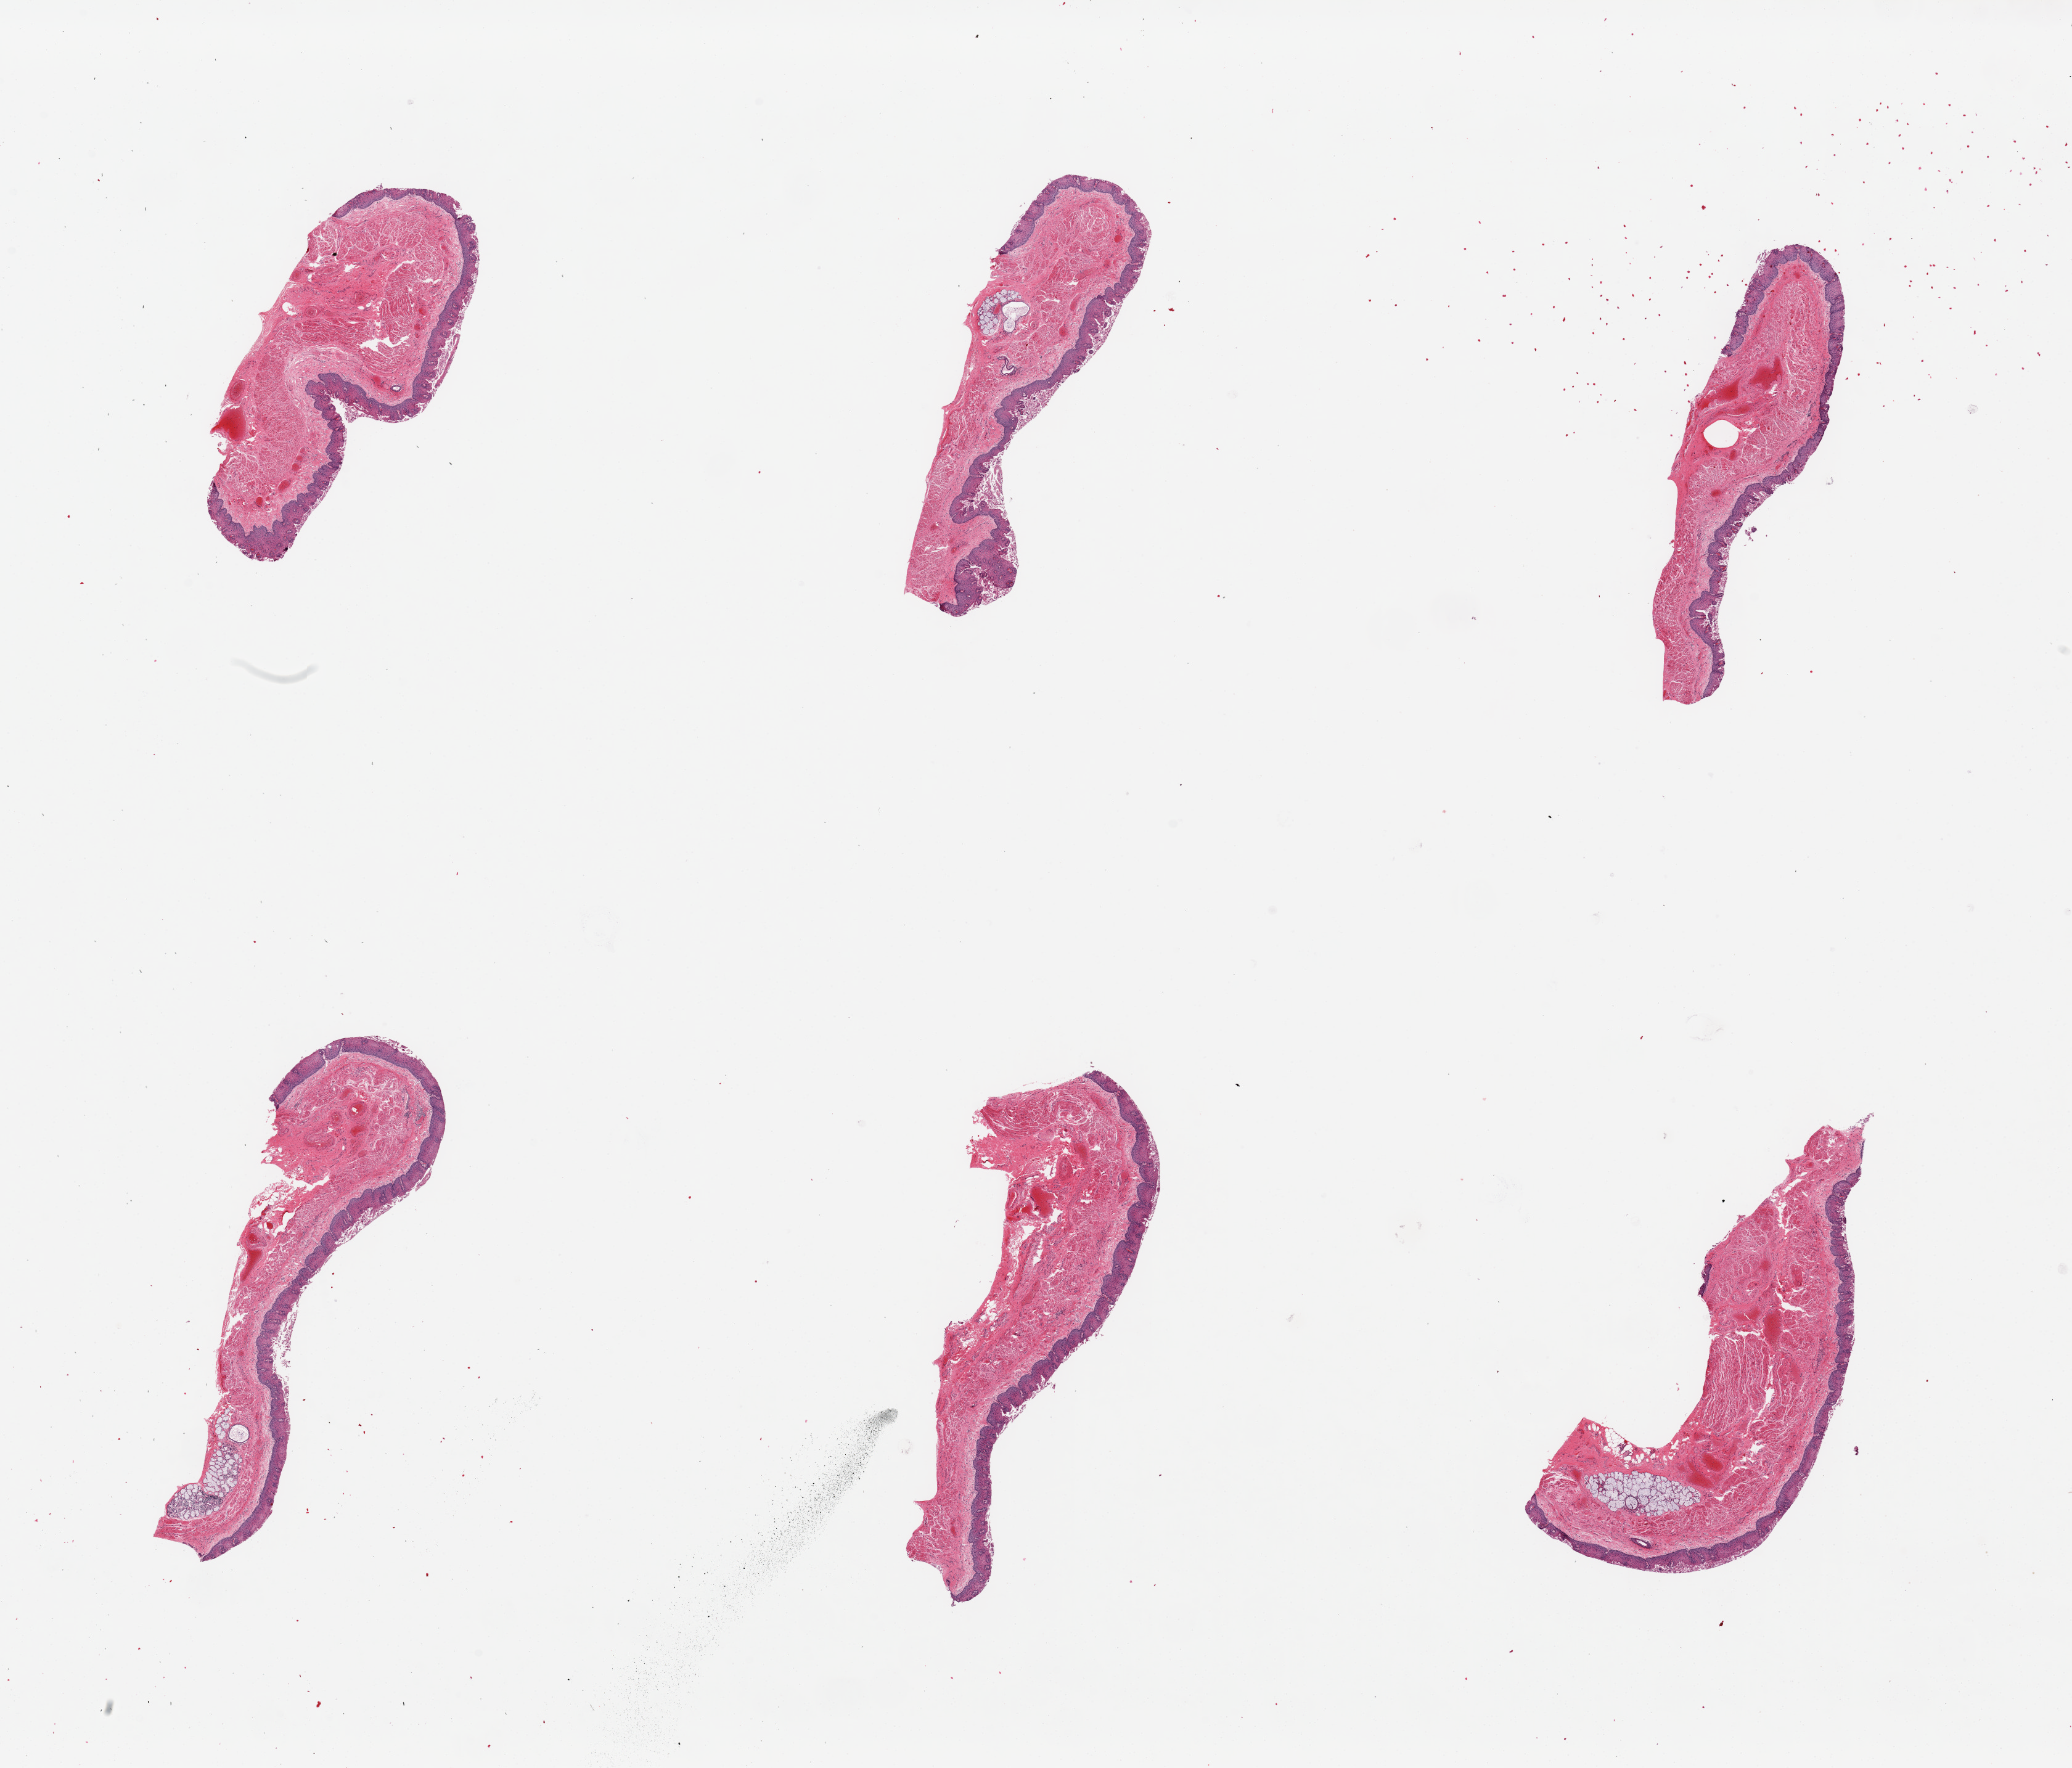
Digitized haematoxylin and eosin-stained section — shown as a low-resolution overview of the whole scanned area (about 26.6 x 22.7 mm, slide scanned at 20x), PAXgene-fixed paraffin-embedded (PFPE) section, target tissue: esophageal mucous membrane, donor tissue sample. Donor sex: male.
* review note (as recorded): 6 pieces ~6x1.5mm. Squamous mucosa is 10-15% thickness, well-preserved